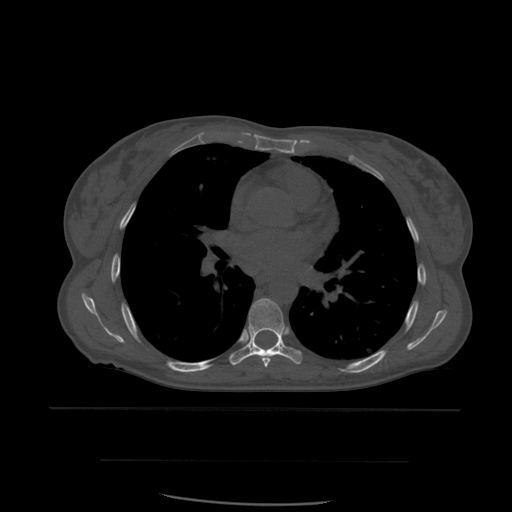
CT including the spine, one axial slice. Position 379 of 574 along the scan axis. Bone window (W 1800 / L 400 HU). 1.25 mm slice thickness. 512 × 512 image matrix. Patient age 48 years. Case-level facts recorded for this patient, not image findings: primary cancer: lung.
Annotated regions visible in this slice (semi-automatically segmented with operator editing):
- T6 vertebra: bounding box <261,357,272,368> (left, top, right, bottom; pixels)
- T7 vertebra: <230,299,302,366>